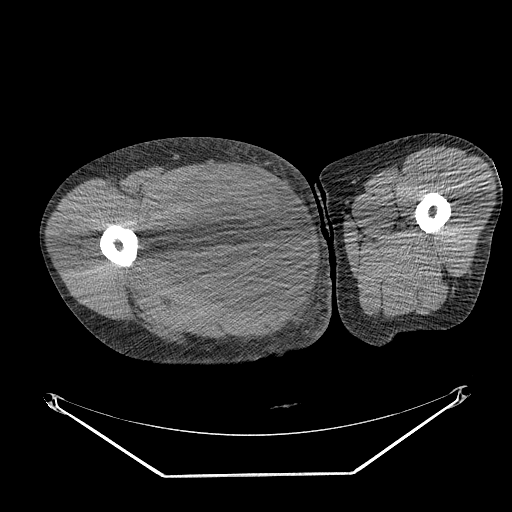
CT of an extremity soft-tissue mass (from a PET/CT study), one axial slice. Position 262 of 311 along the scan axis. Reconstruction kernel STANDARD. 140 kVp. Soft-tissue window (W 400 / L 40 HU). 512 × 512 image matrix. Male patient. From the clinical record (not read from this slice): histological type: undifferentiated - pleiomorphic; grade: high; site of the primary tumour: right thigh.
Annotated regions visible in this slice (expert contour drawn on MRI and transferred to this co-registered scan by the dataset authors):
- gross tumour volume including surrounding oedema: box from (x=146, y=167) to (x=268, y=280) px
- gross tumour volume (mass): (x=155, y=169)–(x=268, y=279)